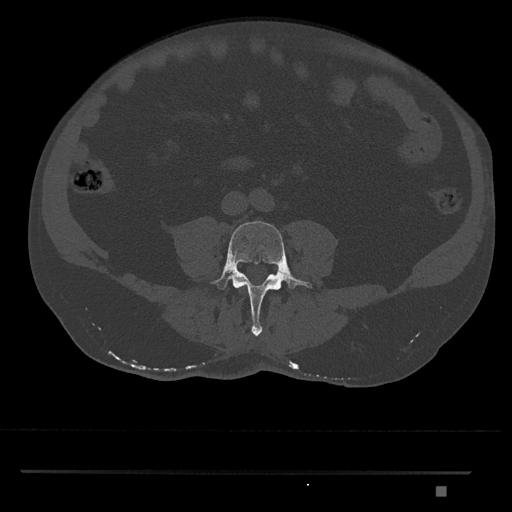
CT including the spine, one axial slice; slice 617 of 1134 in the series (ordered by position); reconstruction kernel Br40s/3; 120 kVp; bone window (W 1800 / L 400 HU); 512 × 512 image matrix, field of view 429 × 429 mm. Patient: male, 65 years. From the clinical record (not read from this slice): primary cancer: prostate.
Structures marked on this image (semi-automatically segmented with operator editing):
- L4 vertebra: bounding box [x1, y1, x2, y2] px = [211, 221, 313, 336]